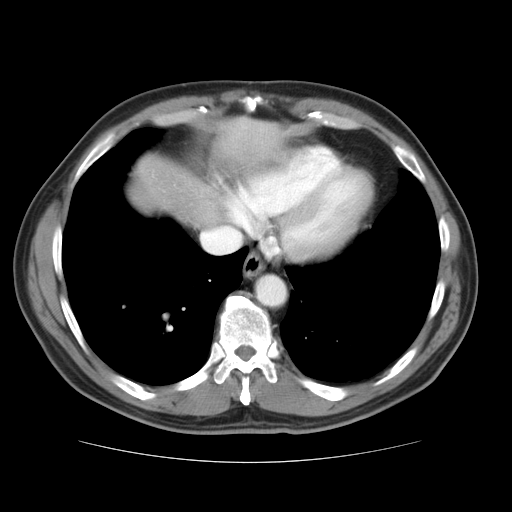
Contrast-enhanced abdominal CT, one axial slice; slice 34 of 37 in the series (ordered by position); 120 kVp; soft-tissue window (W 400 / L 40 HU); 5 mm slice thickness; 512 × 512 image matrix, field of view 374 × 374 mm. Male patient, age 66 years. Case-level facts recorded for this patient, not image findings: diagnosis: colorectal cancer liver metastases, imaged before liver resection; multiple liver metastases: yes; largest metastasis: 1.6 cm.
Annotated regions visible in this slice (expert manual segmentation):
- liver: bounding box <131,120,281,230> (left, top, right, bottom; pixels)
- planned liver remnant (the part of the liver to remain after resection): <138,122,281,230>